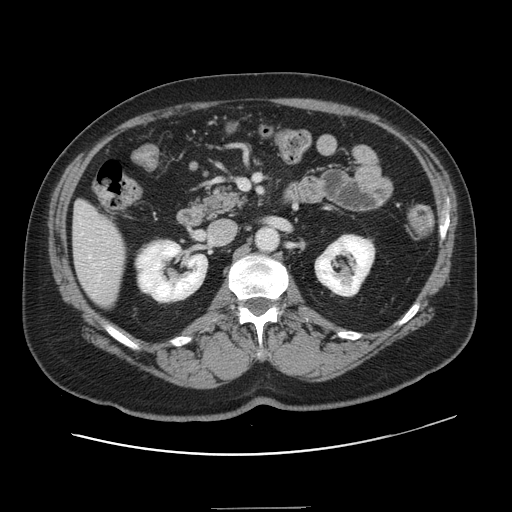
Contrast-enhanced abdominal CT, one axial slice; slice 59 of 143 in the series (ordered by position); intravenous contrast given; soft-tissue window (W 400 / L 40 HU); 2.5 mm slice thickness; 512 × 512 image matrix. Male patient, age 62 years. Case-level facts recorded for this patient, not image findings: diagnosis: colorectal cancer liver metastases, imaged before liver resection; multiple liver metastases: yes; largest metastasis: 2.7 cm; disease in both lobes: no.
Outlined on this slice (manually delineated by an expert):
- hepatic veins: bounding box (x1, y1, x2, y2) in pixels: (89, 256, 95, 267)
- liver: (74, 202, 126, 307)